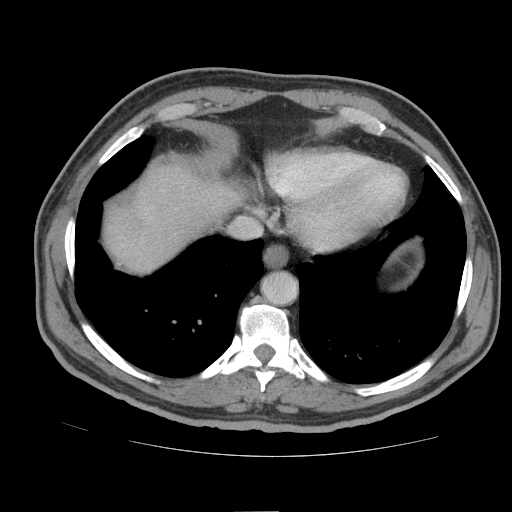
Contrast-enhanced abdominal CT (liver protocol), one axial slice. Position 79 of 105 along the scan axis. Reconstruction kernel STANDARD. 140 kVp. Soft-tissue window (W 400 / L 40 HU). 2.5 mm slice thickness. 512 × 512 image matrix, field of view 380 × 380 mm. Case-level facts recorded for this patient, not image findings: diagnosis: hepatocellular carcinoma (patient treated with transarterial chemoembolisation; whether this scan precedes or follows treatment is not stated here); TNM stage (as recorded): Stage-IIIB; Child-Pugh class: A.
Outlined on this slice (semi-automatically segmented with operator editing):
- liver parenchyma outside the tumour (the mass and vessels are separate outlines, so this box may not span the whole liver): bounding box <104,164,242,272> (left, top, right, bottom; pixels)